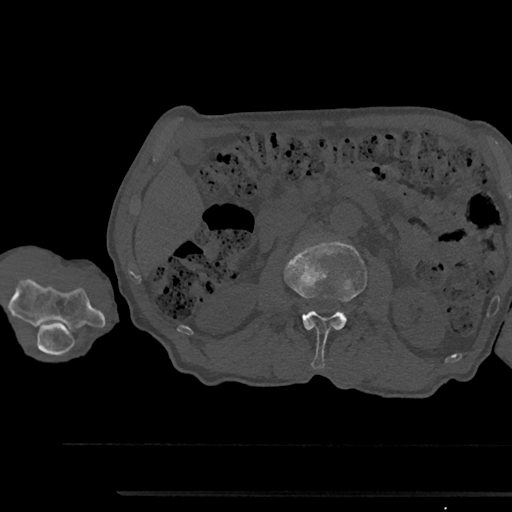
CT including the spine, one axial slice. Position 552 of 797 along the scan axis. Reconstruction kernel Br40s/3. 120 kVp. Bone window (W 1800 / L 400 HU). 0.5 mm slice thickness. 512 × 512 image matrix, field of view 367 × 367 mm. Male patient, age 79 years. From the clinical record (not read from this slice): primary cancer: prostate.
Annotated regions visible in this slice (semi-automatic segmentation, software-assisted and operator-edited):
- L2 vertebra: bounding box <285,241,367,369> (left, top, right, bottom; pixels)